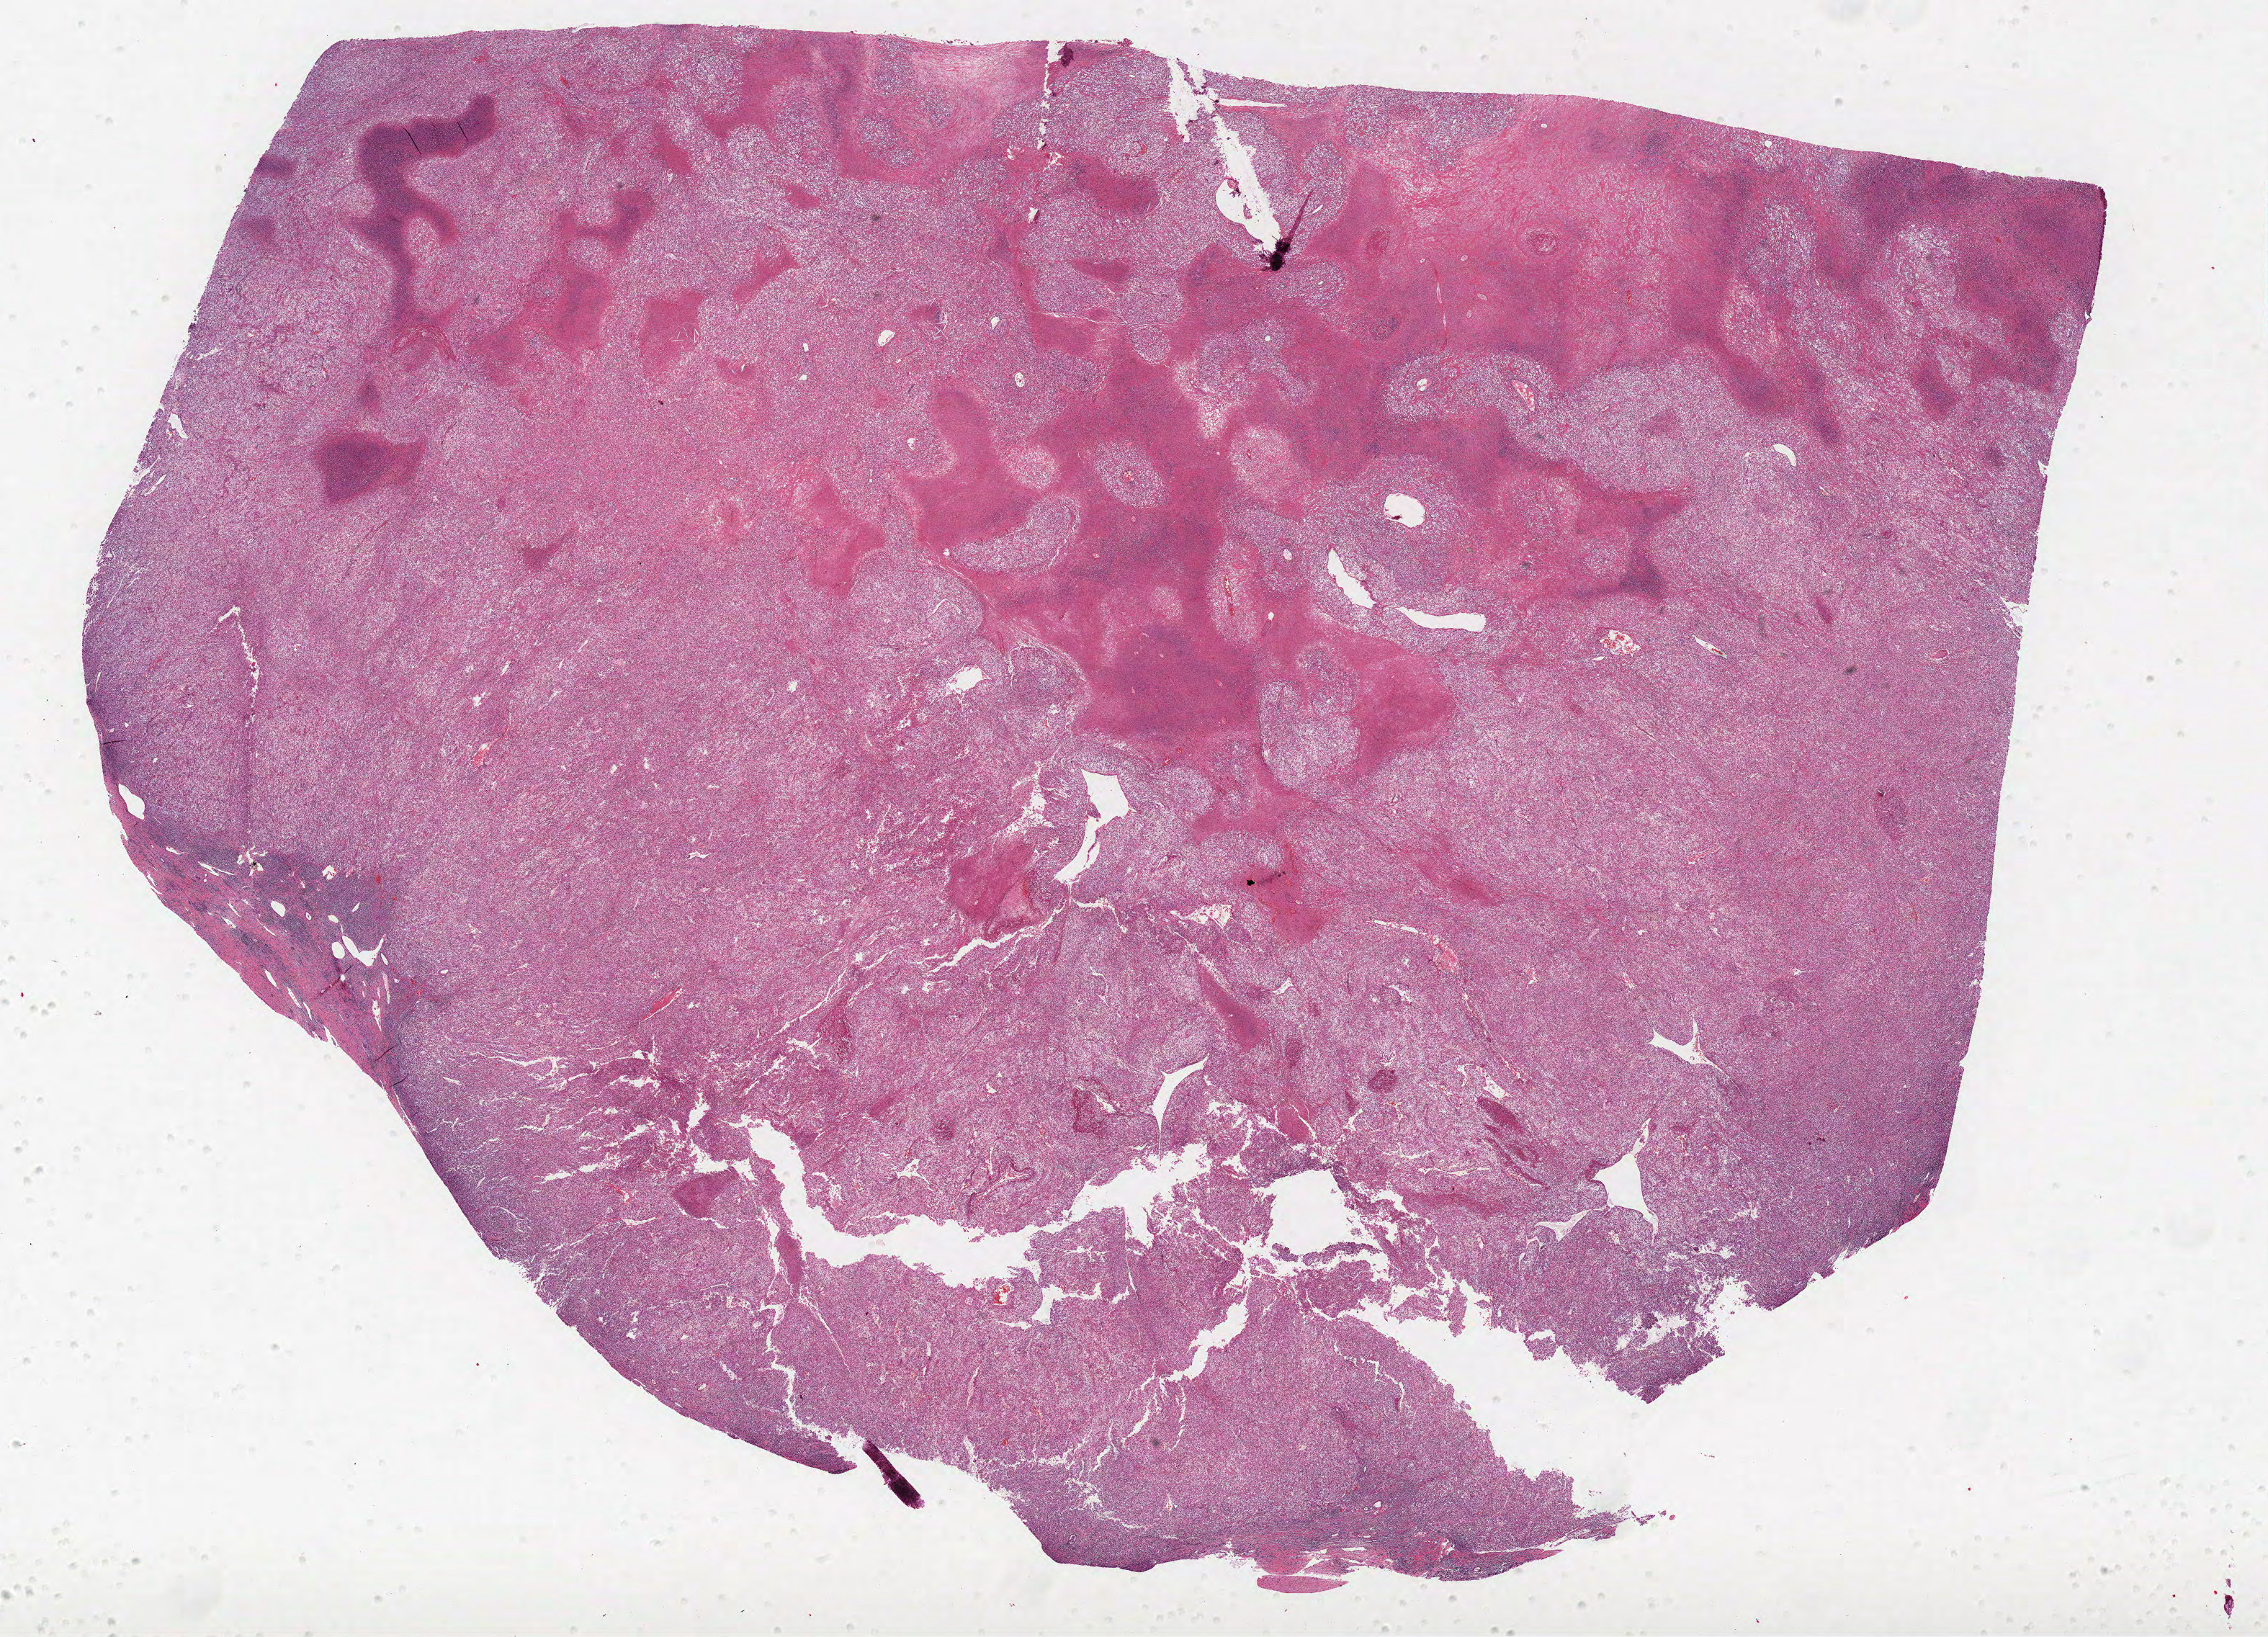
Whole-slide histology image, H&E-stained, whole scanned area (about 25.2 x 18.2 mm, acquisition: 40x scan) shown as a low-resolution overview, FFPE section, sample: primary tumour, kidney. Patient: male, age at initial diagnosis 40 years. Histologic grade: G4 (undifferentiated).
AJCC pathologic stage: IV. Lymph nodes positive (case pathology): 1 of 21 examined. TNM: T4 N1 M1. Pathologic diagnosis: Clear cell adenocarcinoma, NOS. Laterality: left.